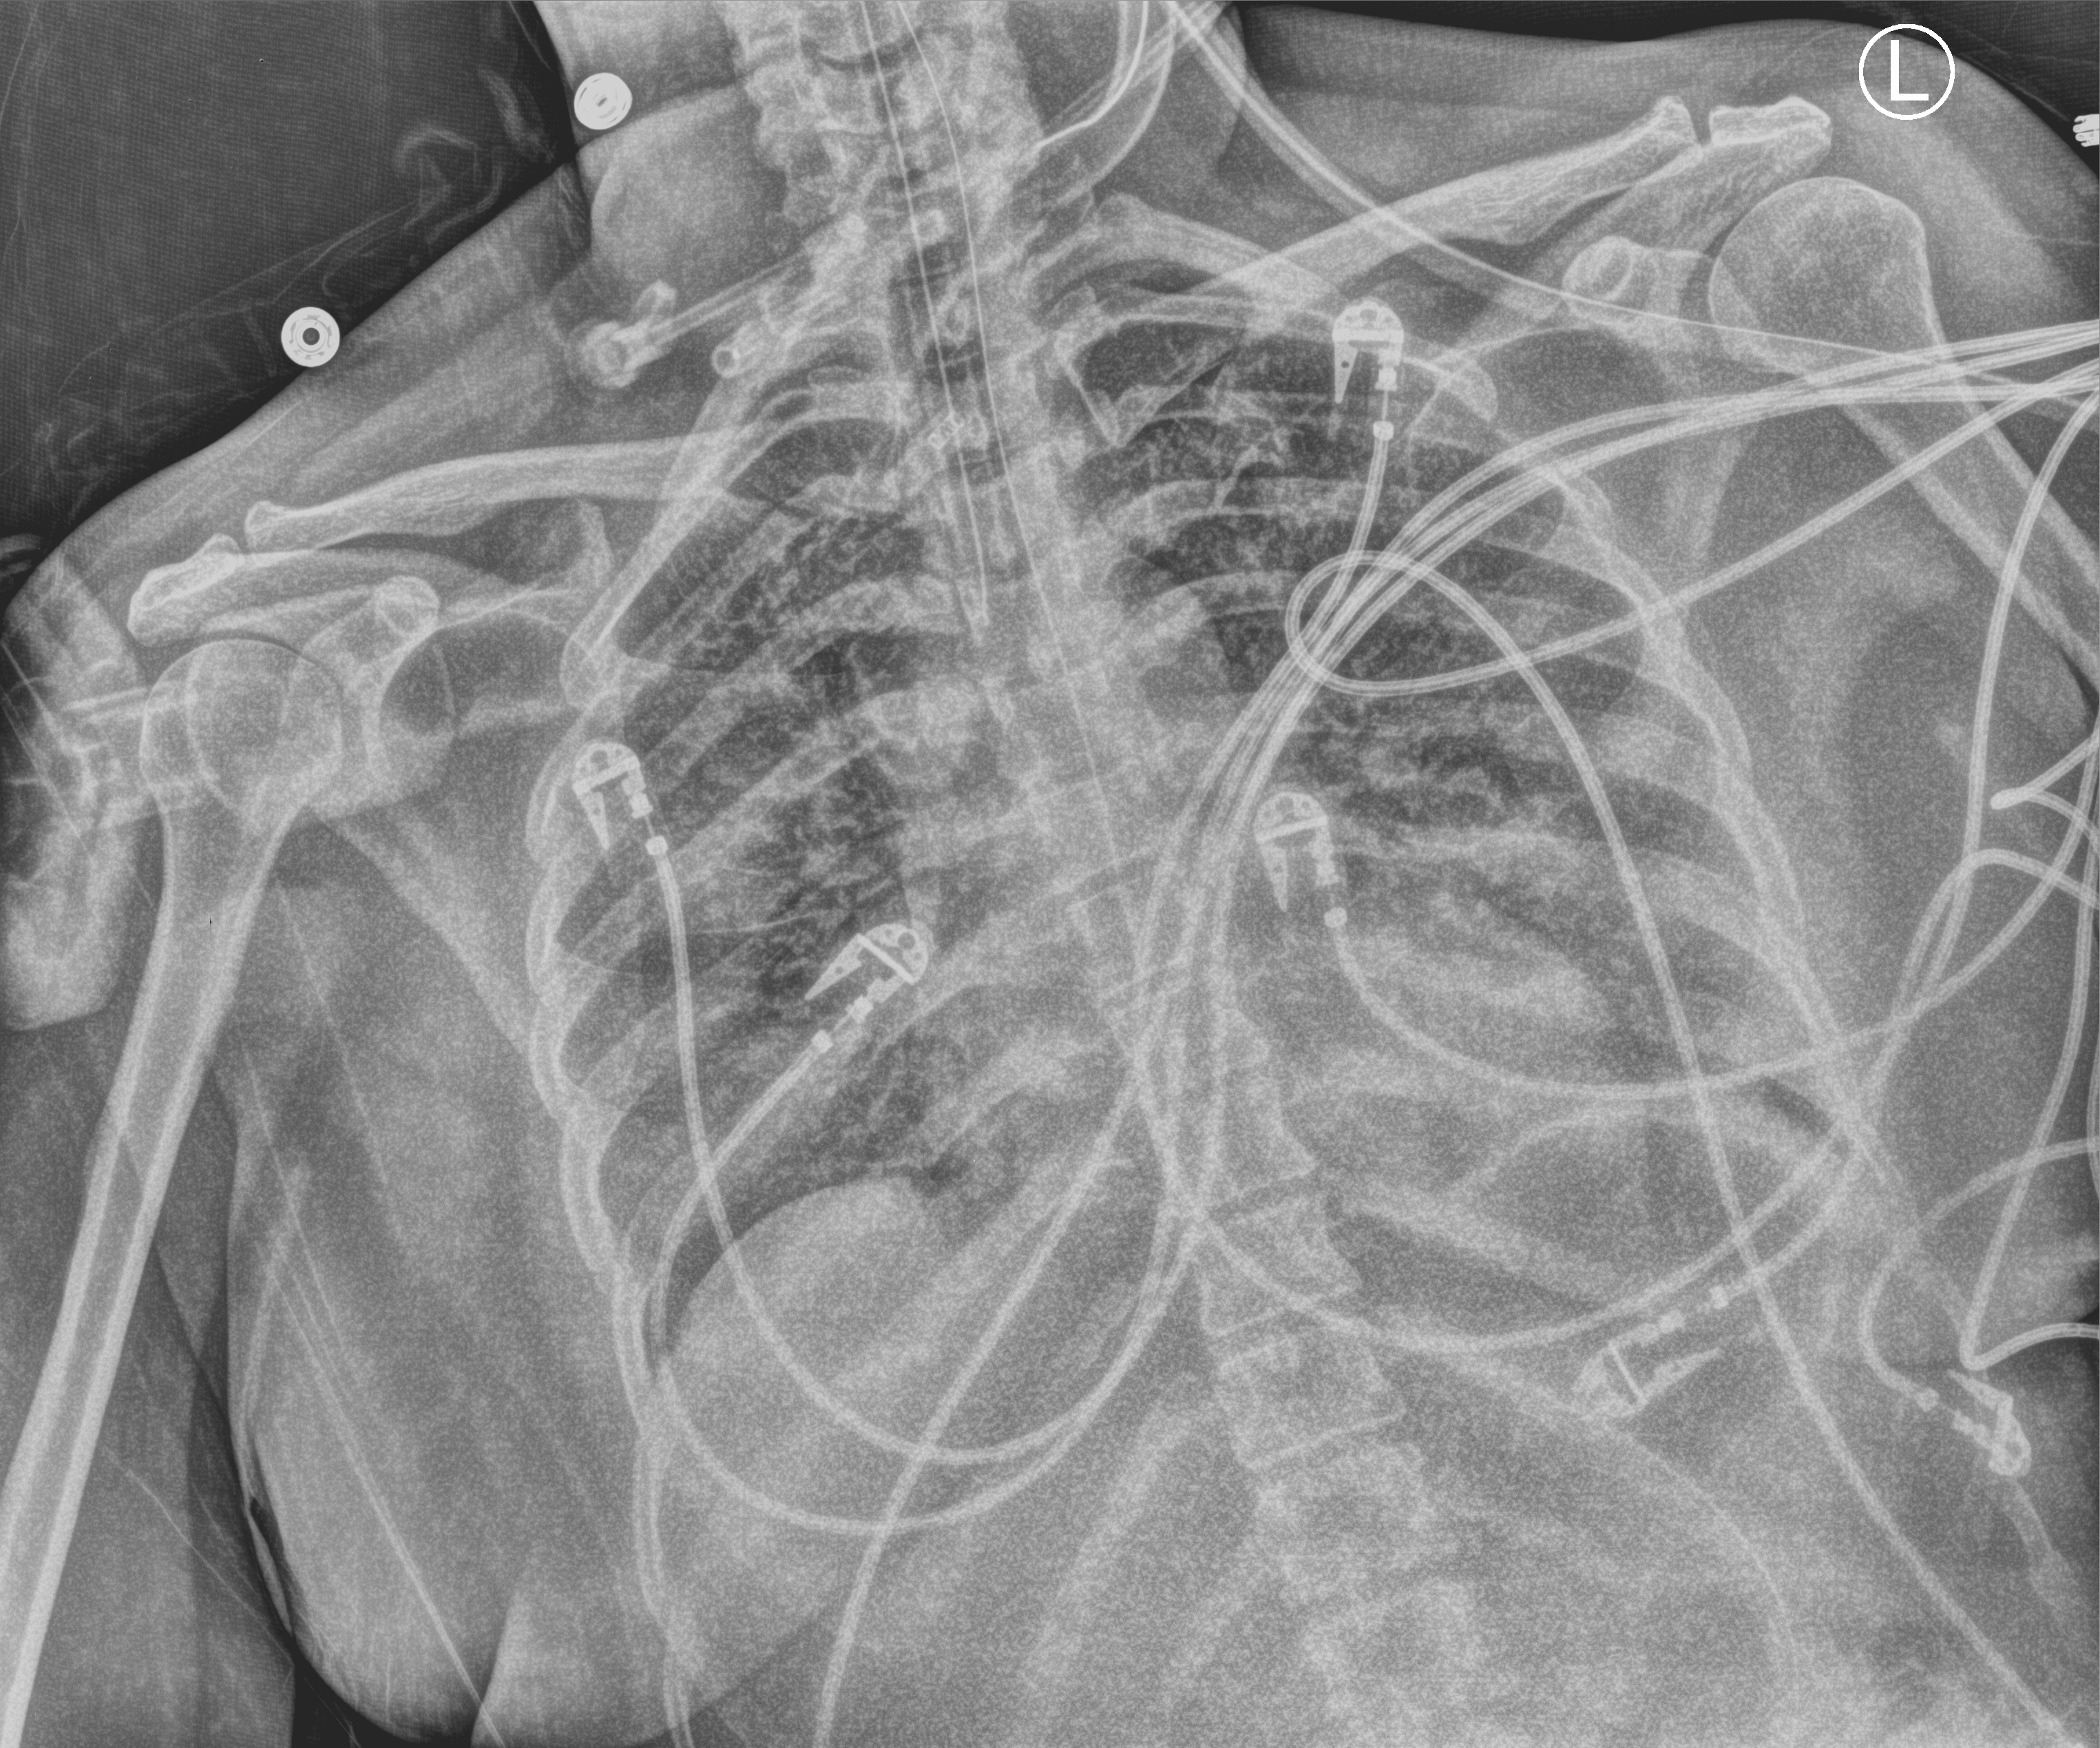
Chest X-ray (portable). Male patient hospitalised with COVID-19, age 18–59 years.
From the hospital-stay record, not from the radiograph (when in the stay this image was taken is not recorded): admitted to intensive care during this hospital stay: yes; mechanically ventilated during this hospital stay: yes.